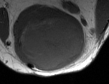
MRI of an extremity soft-tissue mass, one axial slice. MR volume resampled by the dataset authors to the PET/CT grid (not the native acquisition matrix). 3.27 mm slice thickness. 109 × 84 image matrix. Male patient. Case-level facts recorded for this patient, not image findings: histological type: synovial sarcoma; site of the primary tumour: left poplietal fossa.
Structures marked on this image (expert contour drawn on MRI and transferred to this co-registered scan by the dataset authors):
- gross tumour volume (mass): box from (x=14, y=14) to (x=85, y=72) px